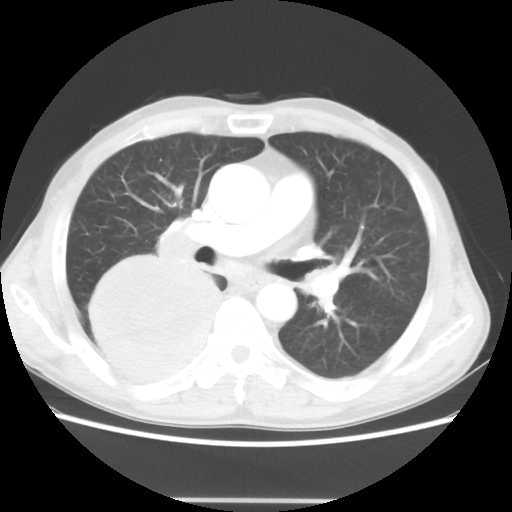
Chest CT, one axial slice; slice 27 of 48 in the series (ordered by position); 100 kVp; lung window (W 1500 / L -600 HU); 5 mm slice thickness; 512 × 512 image matrix, field of view 361 × 361 mm. Patient: male, 66 years. From the clinical record (not read from this slice): clinical TNM (as recorded): T4 N1 M1.
Annotated regions visible in this slice (bounding box drawn by a radiologist):
- lung tumour (recorded histology: small cell carcinoma): box from (x=84, y=246) to (x=225, y=392) px